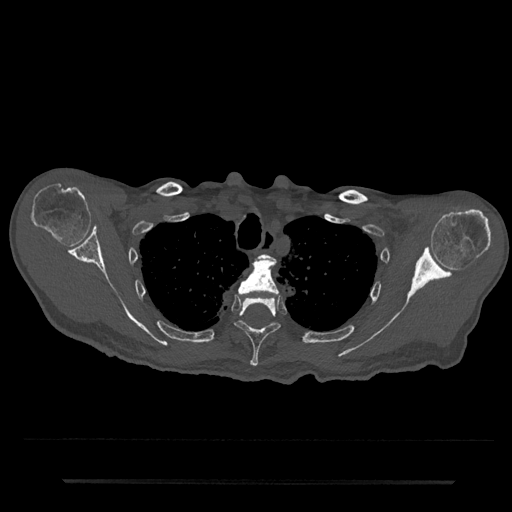
CT including the spine, one axial slice; position 628 of 797 along the scan axis; reconstruction kernel Br40s/3; bone window (W 1800 / L 400 HU); 512 × 512 image matrix, field of view 427 × 427 mm. Patient: male, 74 years. From the clinical record (not read from this slice): primary cancer: prostate.
Annotated regions visible in this slice (semi-automatically segmented with operator editing):
- T2 vertebra: bounding box [x1, y1, x2, y2] px = [259, 254, 270, 260]
- T3 vertebra: [238, 256, 279, 295]
- T4 vertebra: [234, 298, 281, 367]